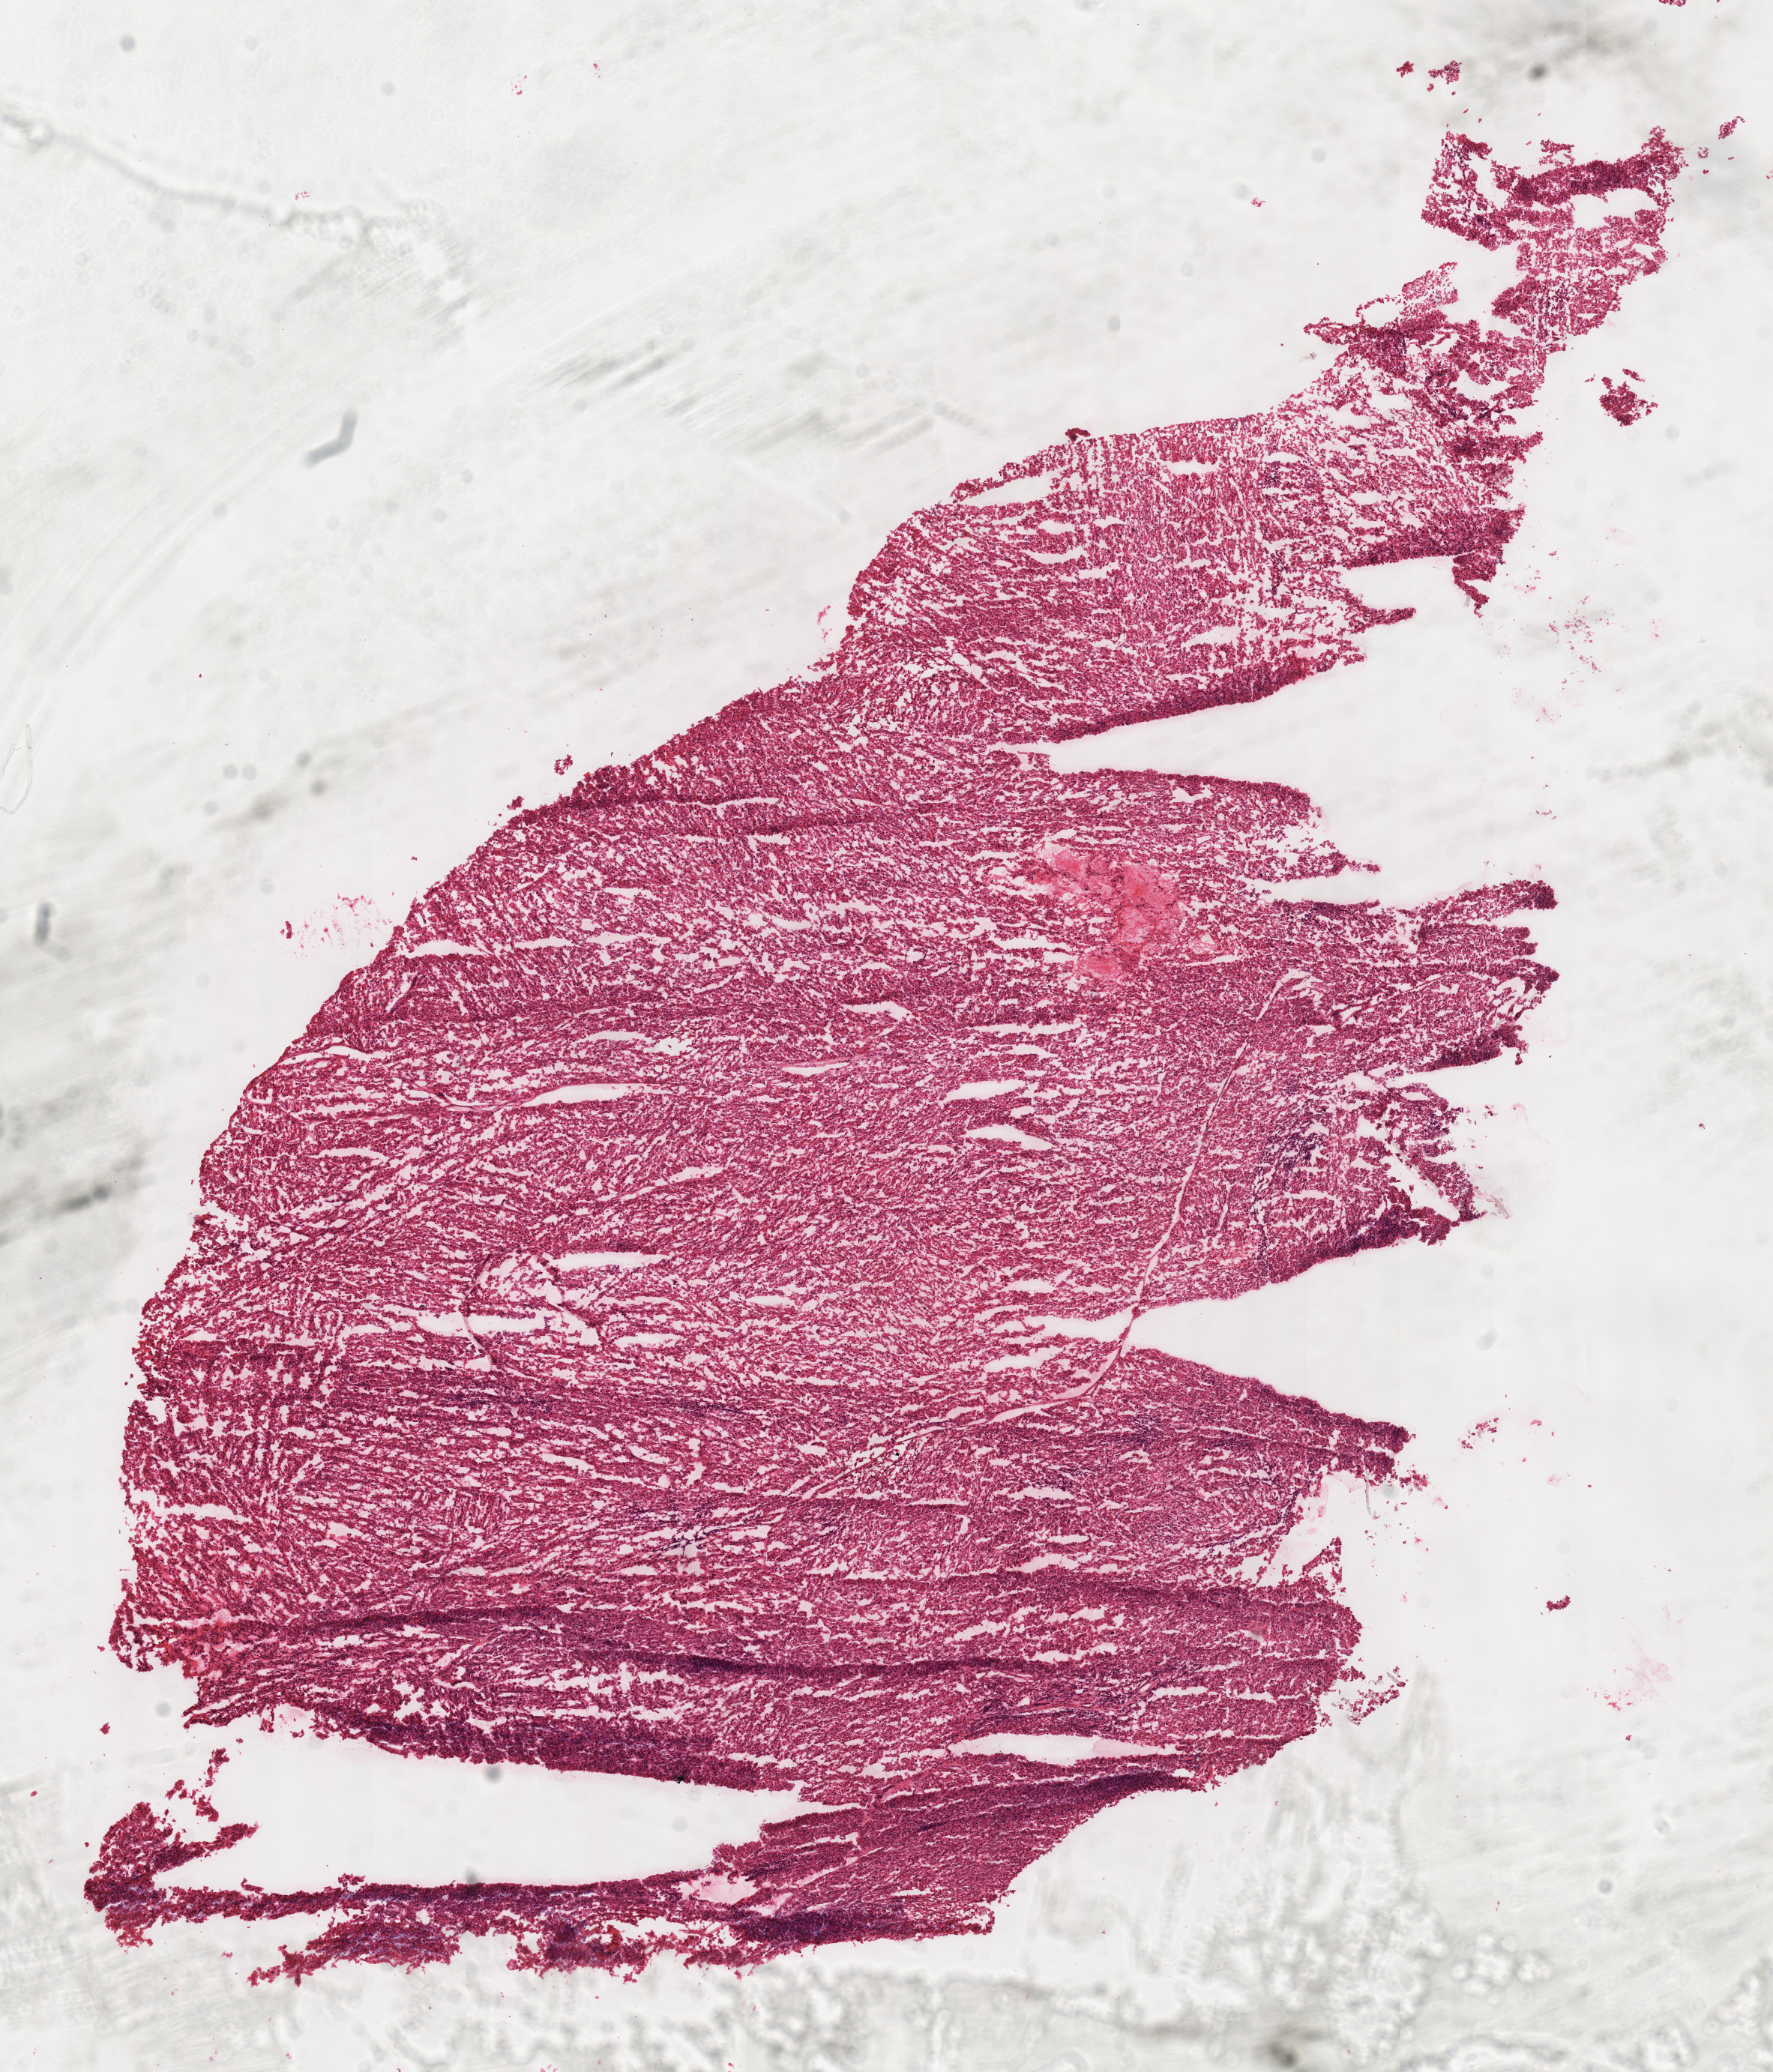
Whole-slide histology image, H&E-stained — whole scanned area (about 9.3 x 10.9 mm, acquisition: 40x scan) shown as a low-resolution overview. Frozen section. Kidney, primary tumour sample. Patient: female, age at initial diagnosis 47 years. Composition of this section per pathologist review: tumour cells 100%, tumour nuclei 95%, normal cells 0%, stromal cells 0%, necrosis 0%. Inflammatory infiltration, as recorded: lymphocyte infiltration 0%, monocyte infiltration 0%, neutrophil infiltration 0%.
AJCC pathologic stage: II (6th edition). Lymph nodes positive (case pathology): 0 of 2 examined. Diagnosis: Renal cell carcinoma, chromophobe type. Laterality: left.